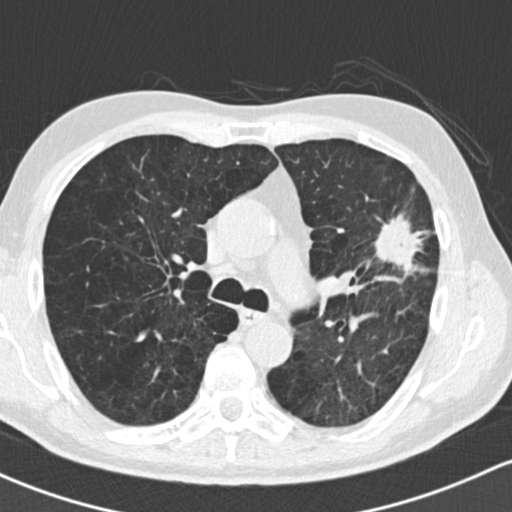
Chest CT (low-dose screening protocol), one axial image. Baseline screening round. Lung window (W 1500 / L -600 HU). Standard (soft-tissue) reconstruction kernel (B30f). Male participant, aged 61 years at enrolment. Former smoker at enrolment.
- Lesion marked by an expert reader, box from (x=356, y=187) to (x=455, y=295) px.
- The exam's reader record, not a measurement of the box and not confirmed to be the same lesion: non-calcified nodule or mass ≥4 mm, left upper lobe, 35 × 35 mm, spiculated (stellate) margins, soft tissue attenuation.
- Official screen result: positive, change unspecified: nodule(s) >= 4 mm or enlarging nodule(s), mass(es), or other non-specific abnormalities suspicious for lung cancer.
- Later outcome: lung cancer diagnosed 19 days after this screen — adenocarcinoma, NOS, left upper lobe, well differentiated (G1), stage IIIA (AJCC 6th edition), 45 mm at pathology.